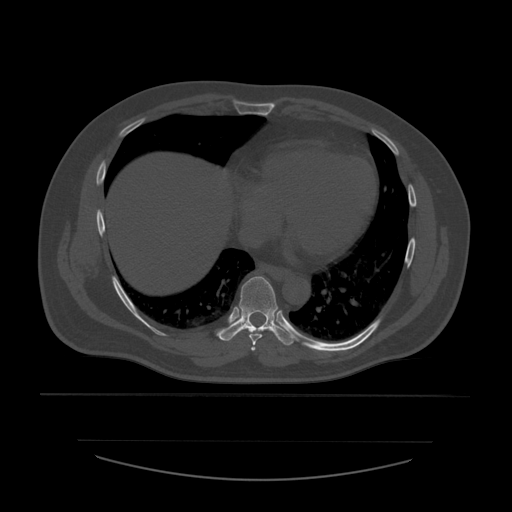
CT including the spine, one axial slice. Slice 344 of 532 in the series (ordered by position). Bone window (W 1800 / L 400 HU). 512 × 512 image matrix, field of view 441 × 441 mm. Patient age 44 years. Case-level facts recorded for this patient, not image findings: primary cancer: soft tissue sarcoma.
Annotated regions visible in this slice (semi-automatic segmentation, software-assisted and operator-edited):
- T6 vertebra: bounding box [x1, y1, x2, y2] px = [251, 347, 256, 353]
- T7 vertebra: [249, 333, 263, 346]
- T8 vertebra: [217, 277, 299, 346]